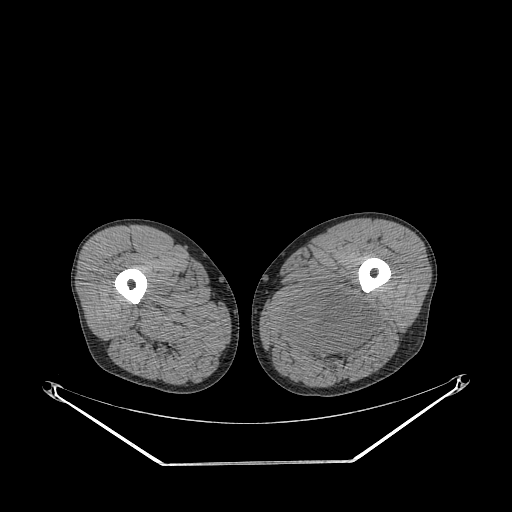
CT of an extremity soft-tissue mass (from a PET/CT study), one axial slice; slice 249 of 267 in the series (ordered by position); reconstruction kernel STANDARD; 140 kVp; soft-tissue window (W 400 / L 40 HU); 512 × 512 image matrix, field of view 500 × 500 mm. Male patient. Case-level facts recorded for this patient, not image findings: histological type: undifferentiated pleomorphic liposarcoma; grade: high; site of the primary tumour: left thigh.
Annotated regions visible in this slice (expert contour drawn on MRI and transferred to this co-registered scan by the dataset authors):
- gross tumour volume including surrounding oedema: bounding box (x1, y1, x2, y2) in pixels: (279, 288, 375, 359)
- gross tumour volume (mass): (290, 288, 375, 350)